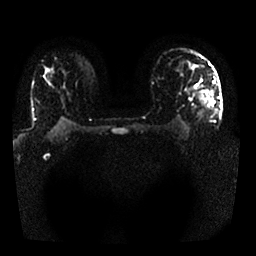
Breast MRI, one axial slice; slice 20 of 25 in the series (ordered by position); diffusion-weighted series; image 2 of 4 stored at this slice position (different b-values; order by instance number); 1.5 T; 4 mm slice thickness; 256 × 256 image matrix, field of view 340 × 340 mm. Female patient.
Outlined on this slice (outlined manually by an expert reader):
- tumour on diffusion-weighted imaging: box from (x=210, y=98) to (x=214, y=104) px